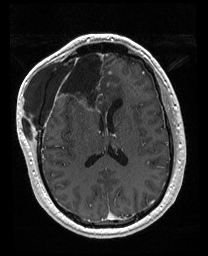
Brain MRI from a brain-tumour surgery series, one axial slice. T1-weighted post-contrast. 1 mm slice thickness. 208 × 256 image matrix, field of view 208 × 256 mm. Case-level facts recorded for this patient, not image findings: histopathology: Astrocytoma; WHO grade: 4; IDH mutation: yes; tumour location: Right Orbitofrontal Anterior Temporal Insular.
Annotated regions visible in this slice (manually delineated by an expert):
- previous resection cavity: bounding box (x1, y1, x2, y2) in pixels: (56, 52, 106, 111)